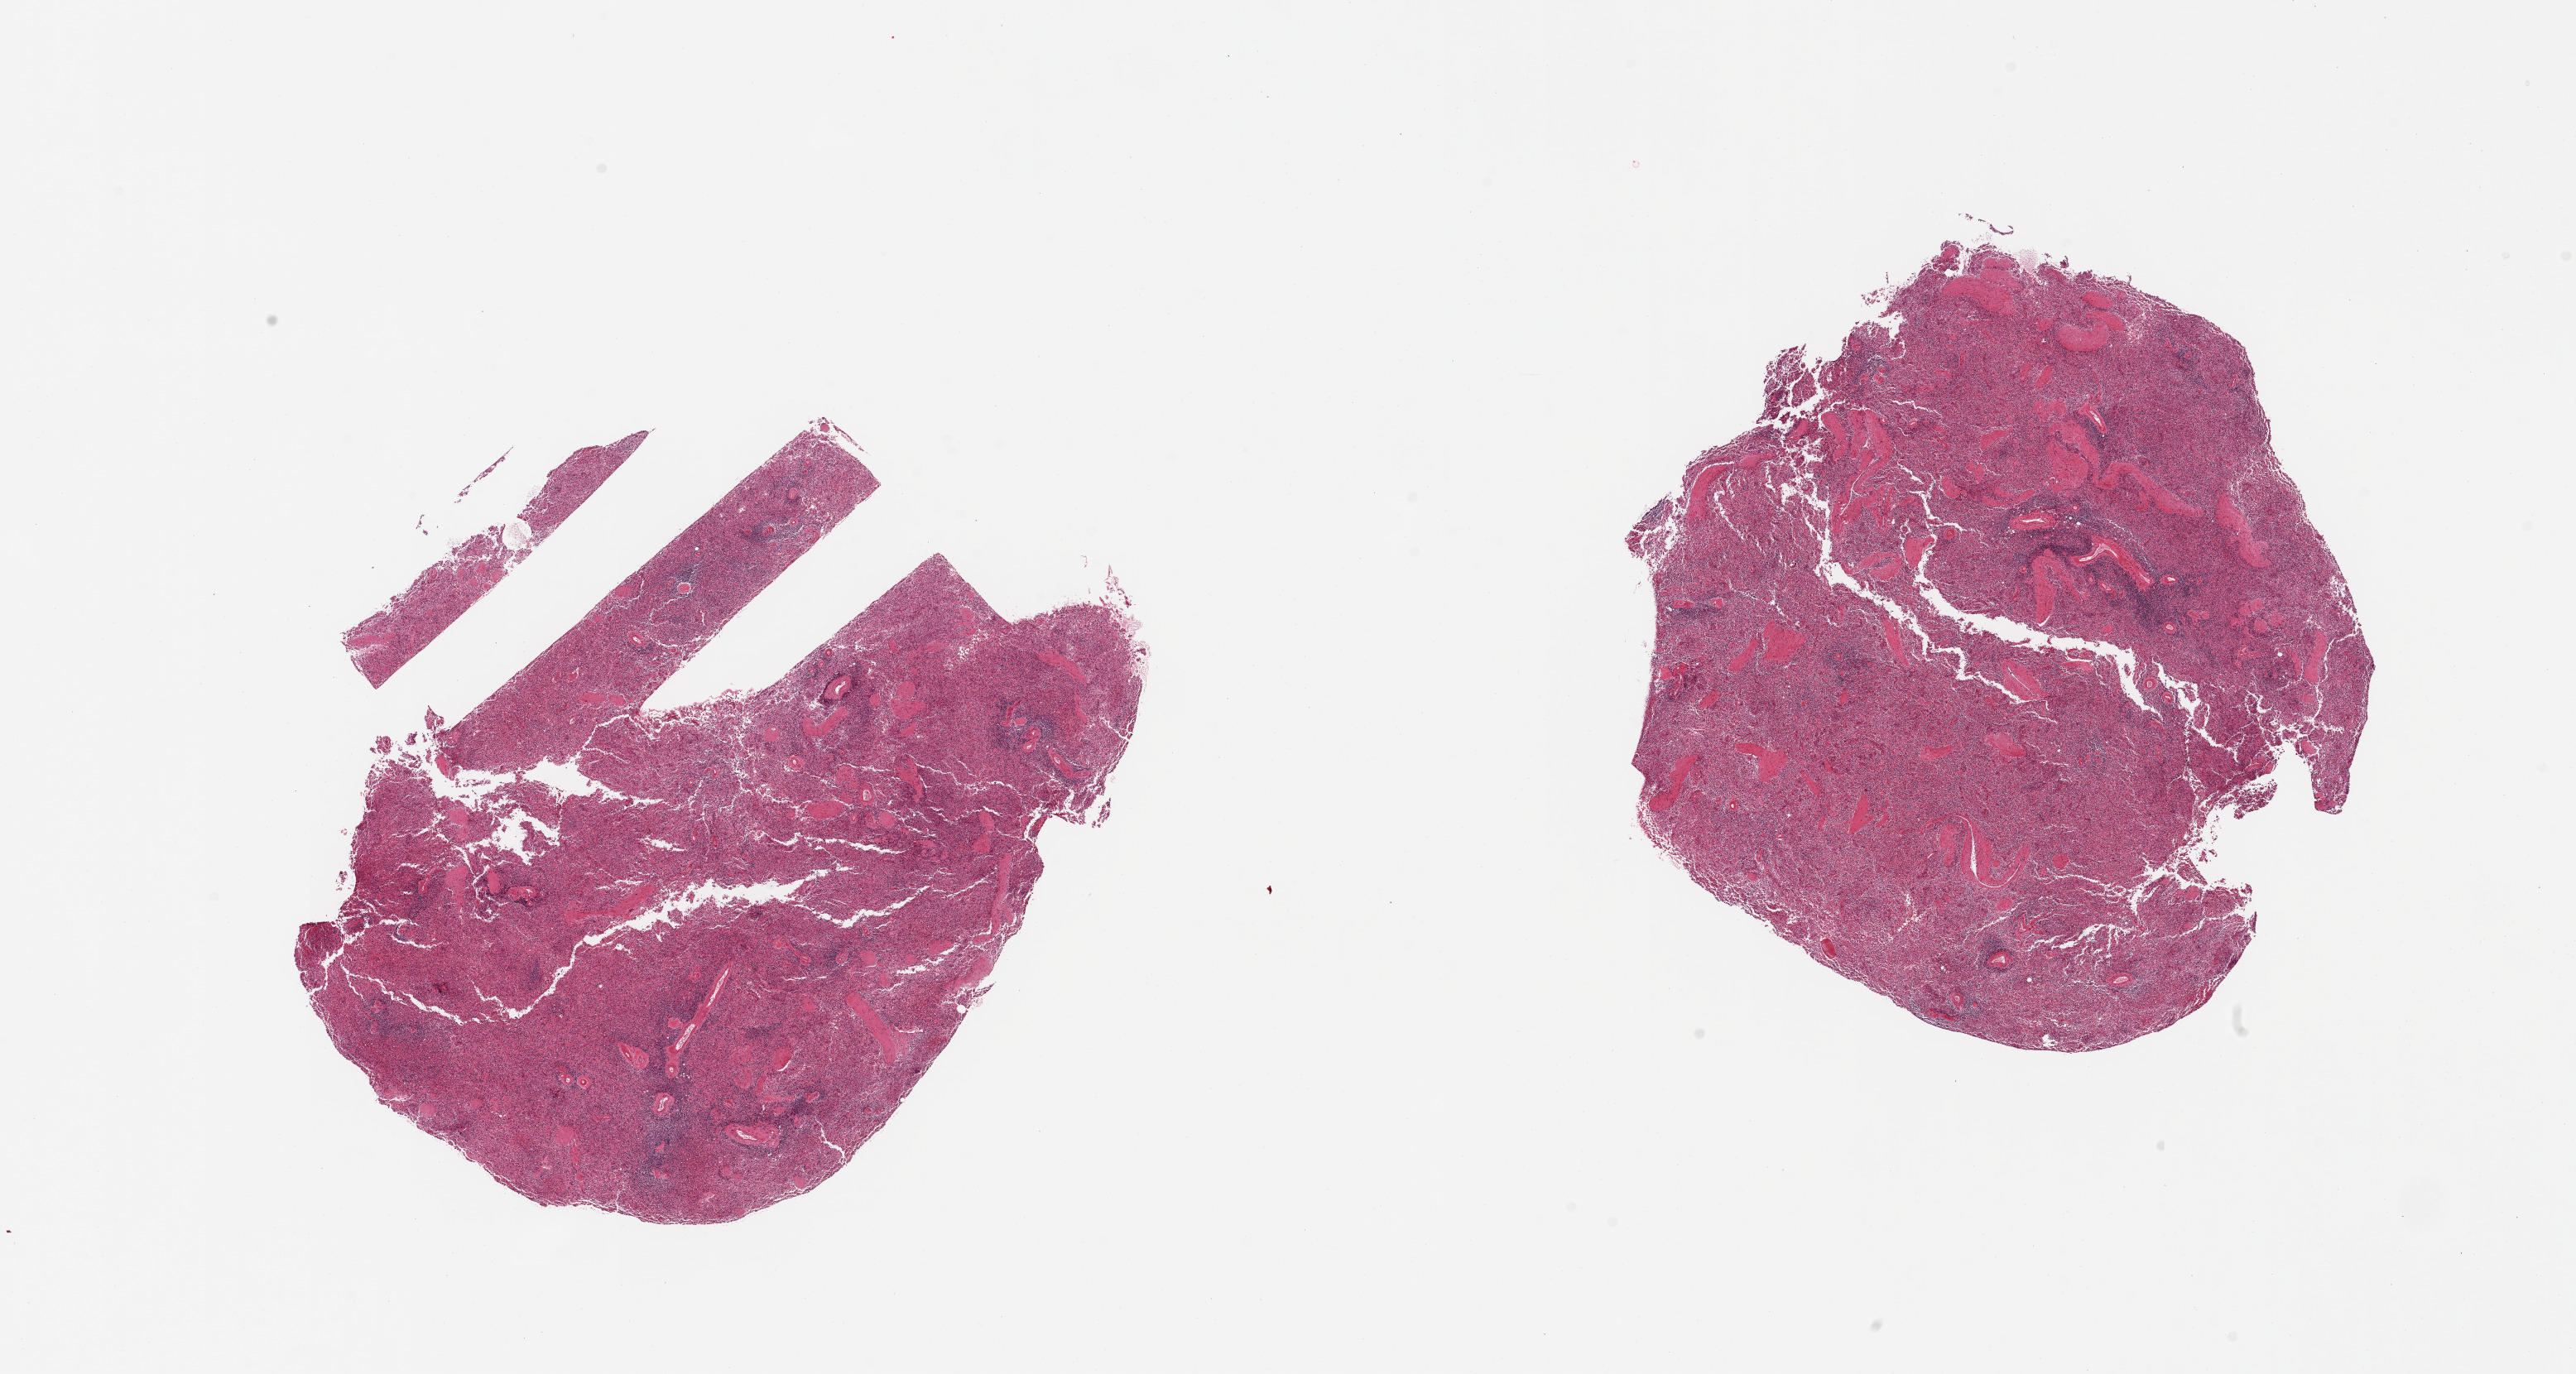
Whole-slide image, haematoxylin and eosin stain, brightfield — shown as a low-resolution overview of the whole scanned area (about 24.6 x 13.1 mm, acquisition: 20x scan), PAXgene-fixed paraffin-embedded (PFPE) section, sampled site (target tissue): spleen, tissue donor sample. Male donor.
Reviewer comment on this tissue sample: 2 pieces, red pulp depletion.